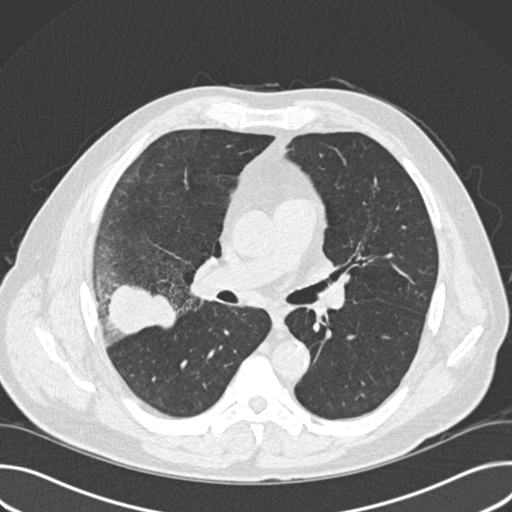
Low-dose screening chest CT, one axial slice. Slice 94 of 157 in the series (ordered by position). Reconstruction kernel B30f. Lung window (W 1500 / L -600 HU). 2 mm slice thickness. 512 × 512 image matrix, field of view 380 × 380 mm.
Annotated regions visible in this slice (expert manual segmentation):
- lesion 1 (tumor, upper lobe of right lung): bounding box <107,285,178,335> (left, top, right, bottom; pixels)